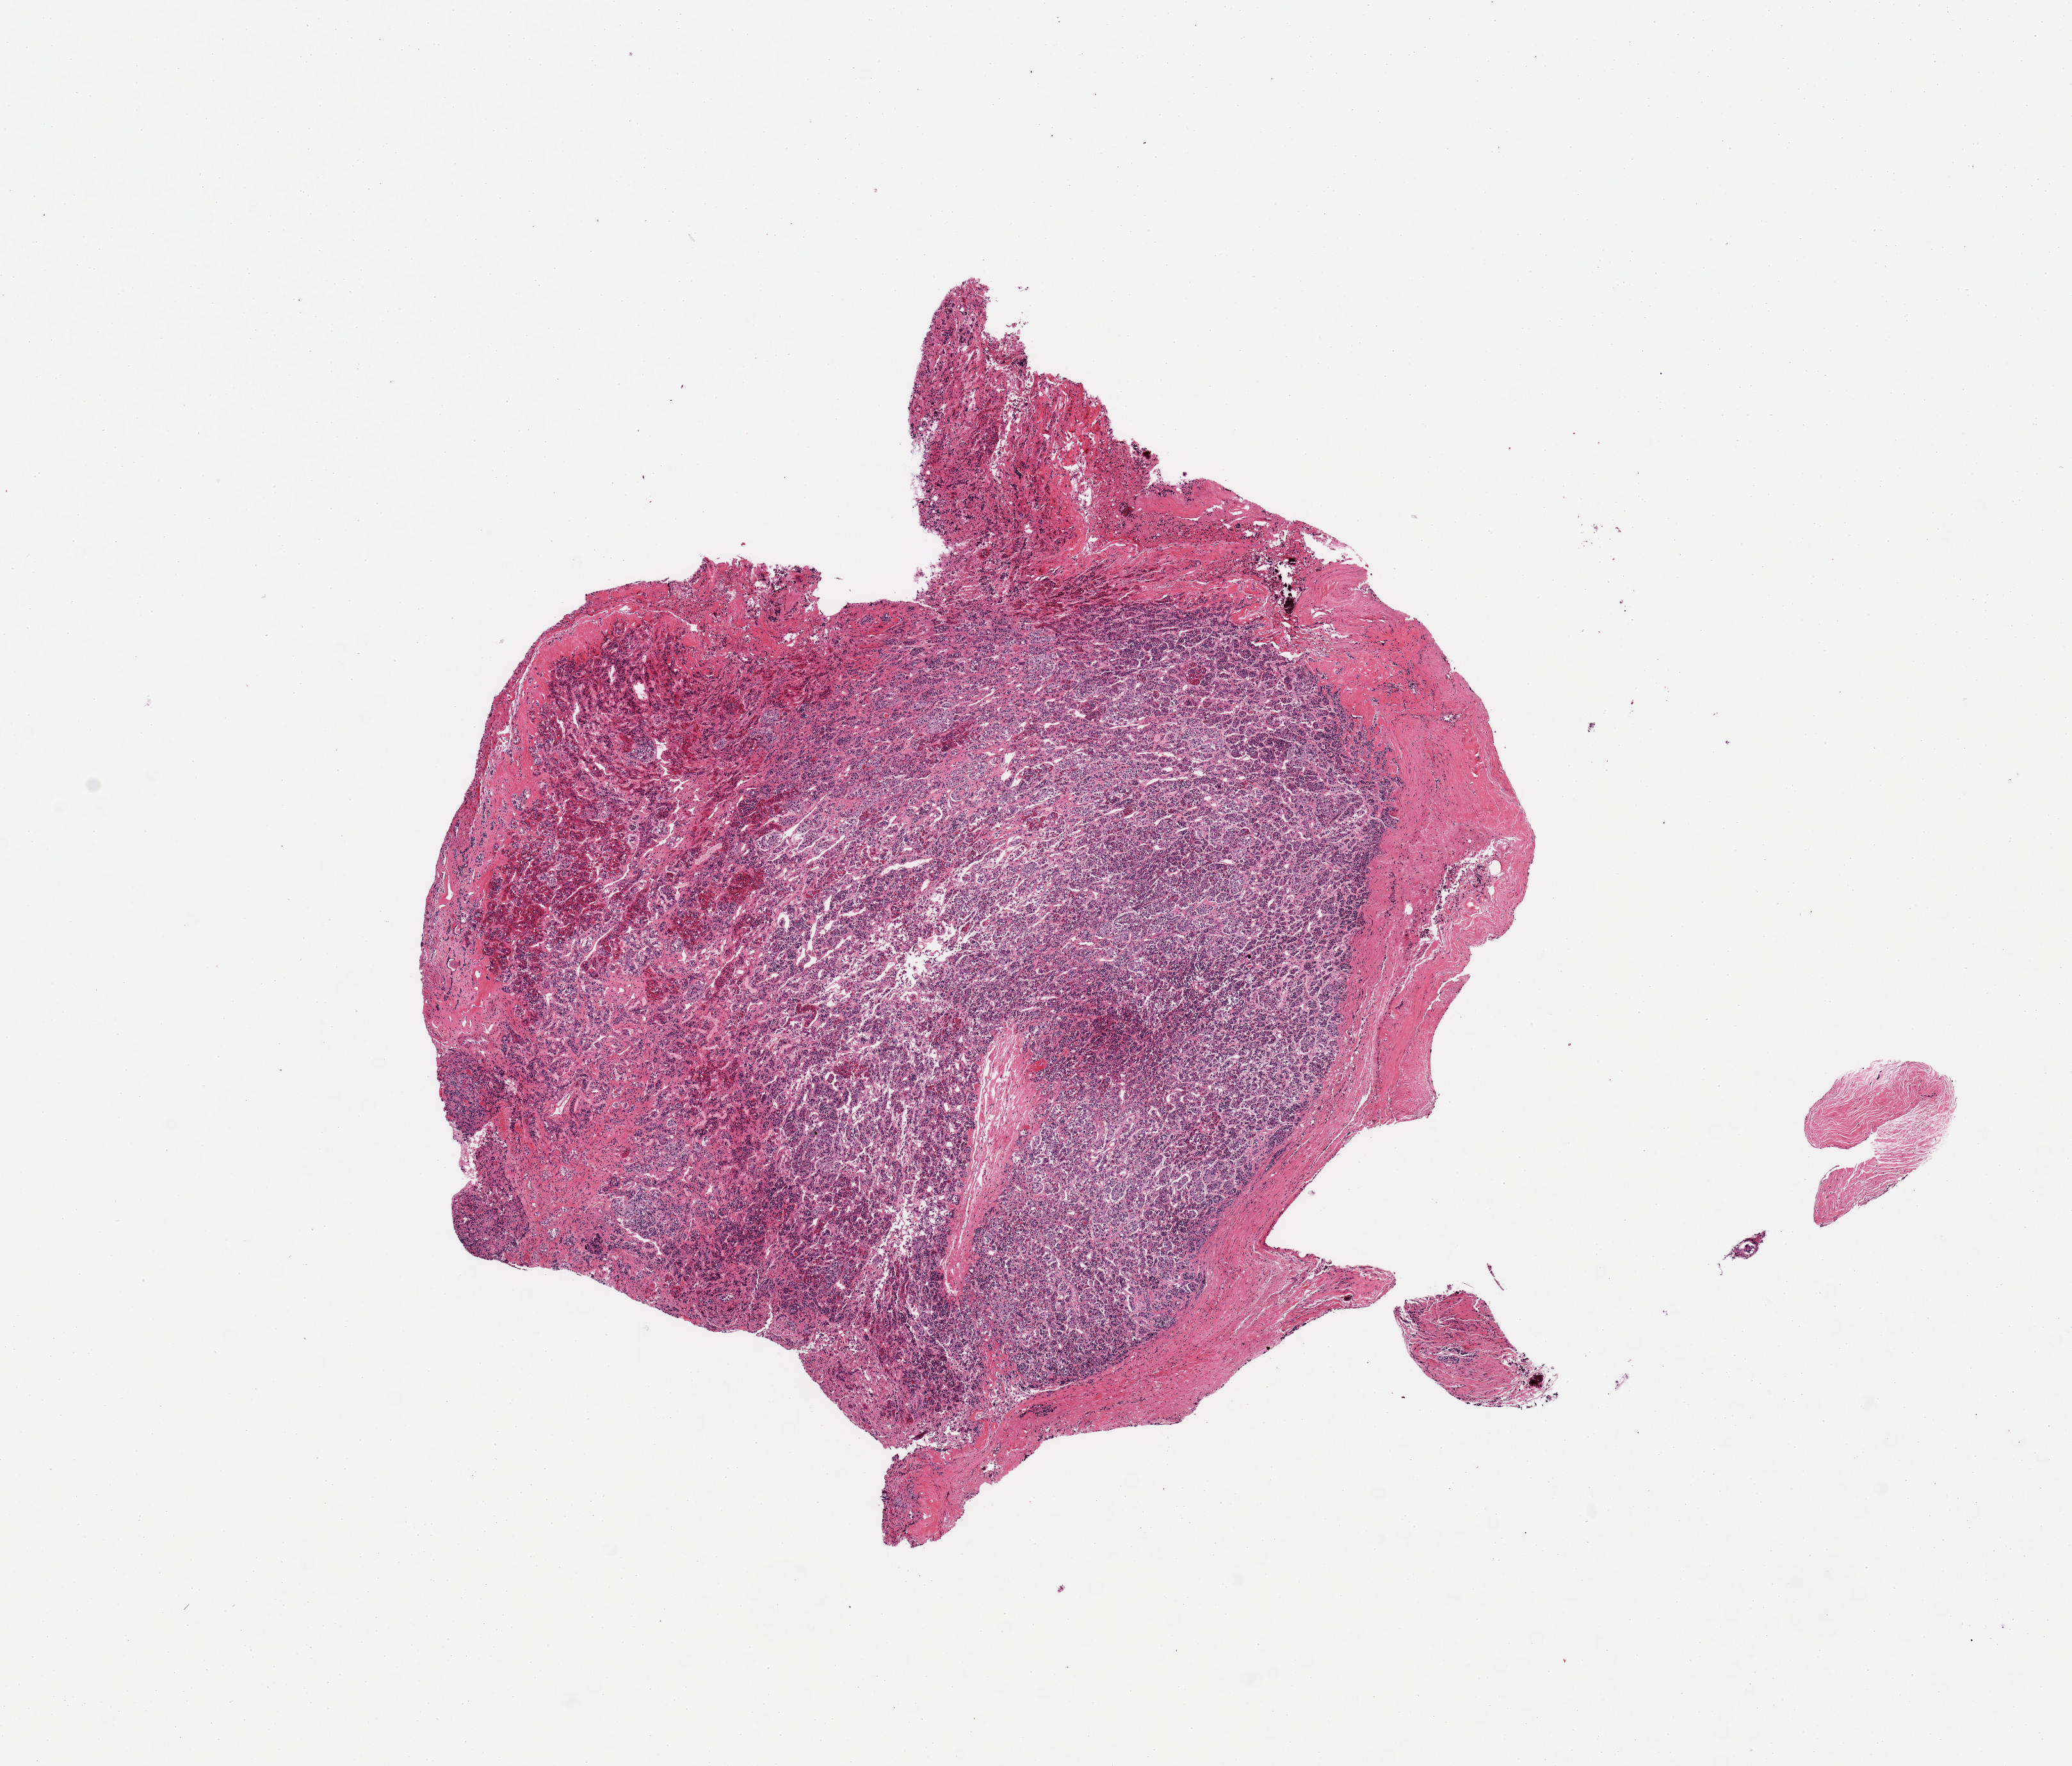
Whole-slide image, hematoxylin and eosin (H&E) stain, whole scanned area (about 12.8 x 10.9 mm) shown as a low-resolution overview; PAXgene-fixed paraffin-embedded (PFPE) section; sampled site (target tissue): pituitary; tissue donor sample. Donor sex: male.
Reviewer comment on this tissue sample: 1 piece, adenohypophysis, rim of dura up to ~0.7mm.